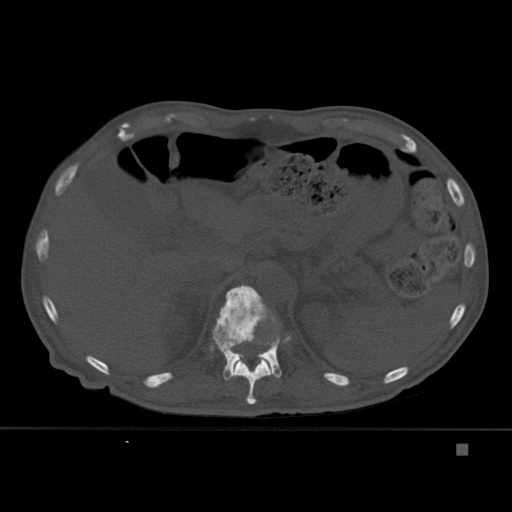
CT including the spine, one axial slice; position 208 of 451 along the scan axis; bone window (W 1800 / L 400 HU); 1.5 mm slice thickness; 512 × 512 image matrix, field of view 378 × 378 mm. Male patient, age 75 years. From the clinical record (not read from this slice): primary cancer: prostate.
Outlined on this slice (semi-automatically segmented with operator editing):
- T11 vertebra: bounding box <233,315,274,405> (left, top, right, bottom; pixels)
- T12 vertebra: <212,284,282,380>